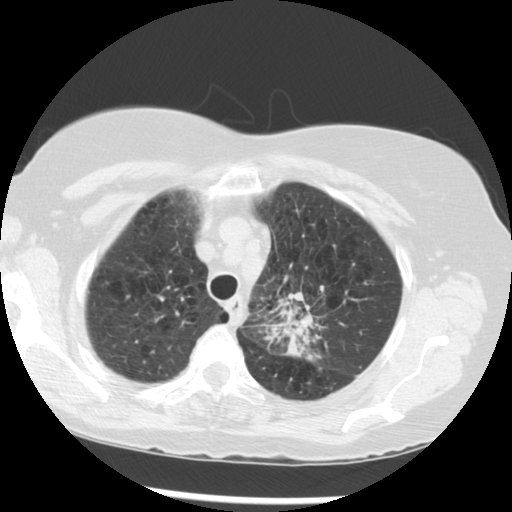
Low-dose screening chest CT, one axial slice; slice 227 of 283 in the series (ordered by position); reconstruction kernel STANDARD; 120 kVp; lung window (W 1500 / L -600 HU); 2.5 mm slice thickness; 512 × 512 image matrix, field of view 330 × 330 mm.
Annotated regions visible in this slice (outlined manually by an expert reader):
- lesion 1 (tumor, upper lobe of left lung): box from (x=277, y=291) to (x=325, y=364) px